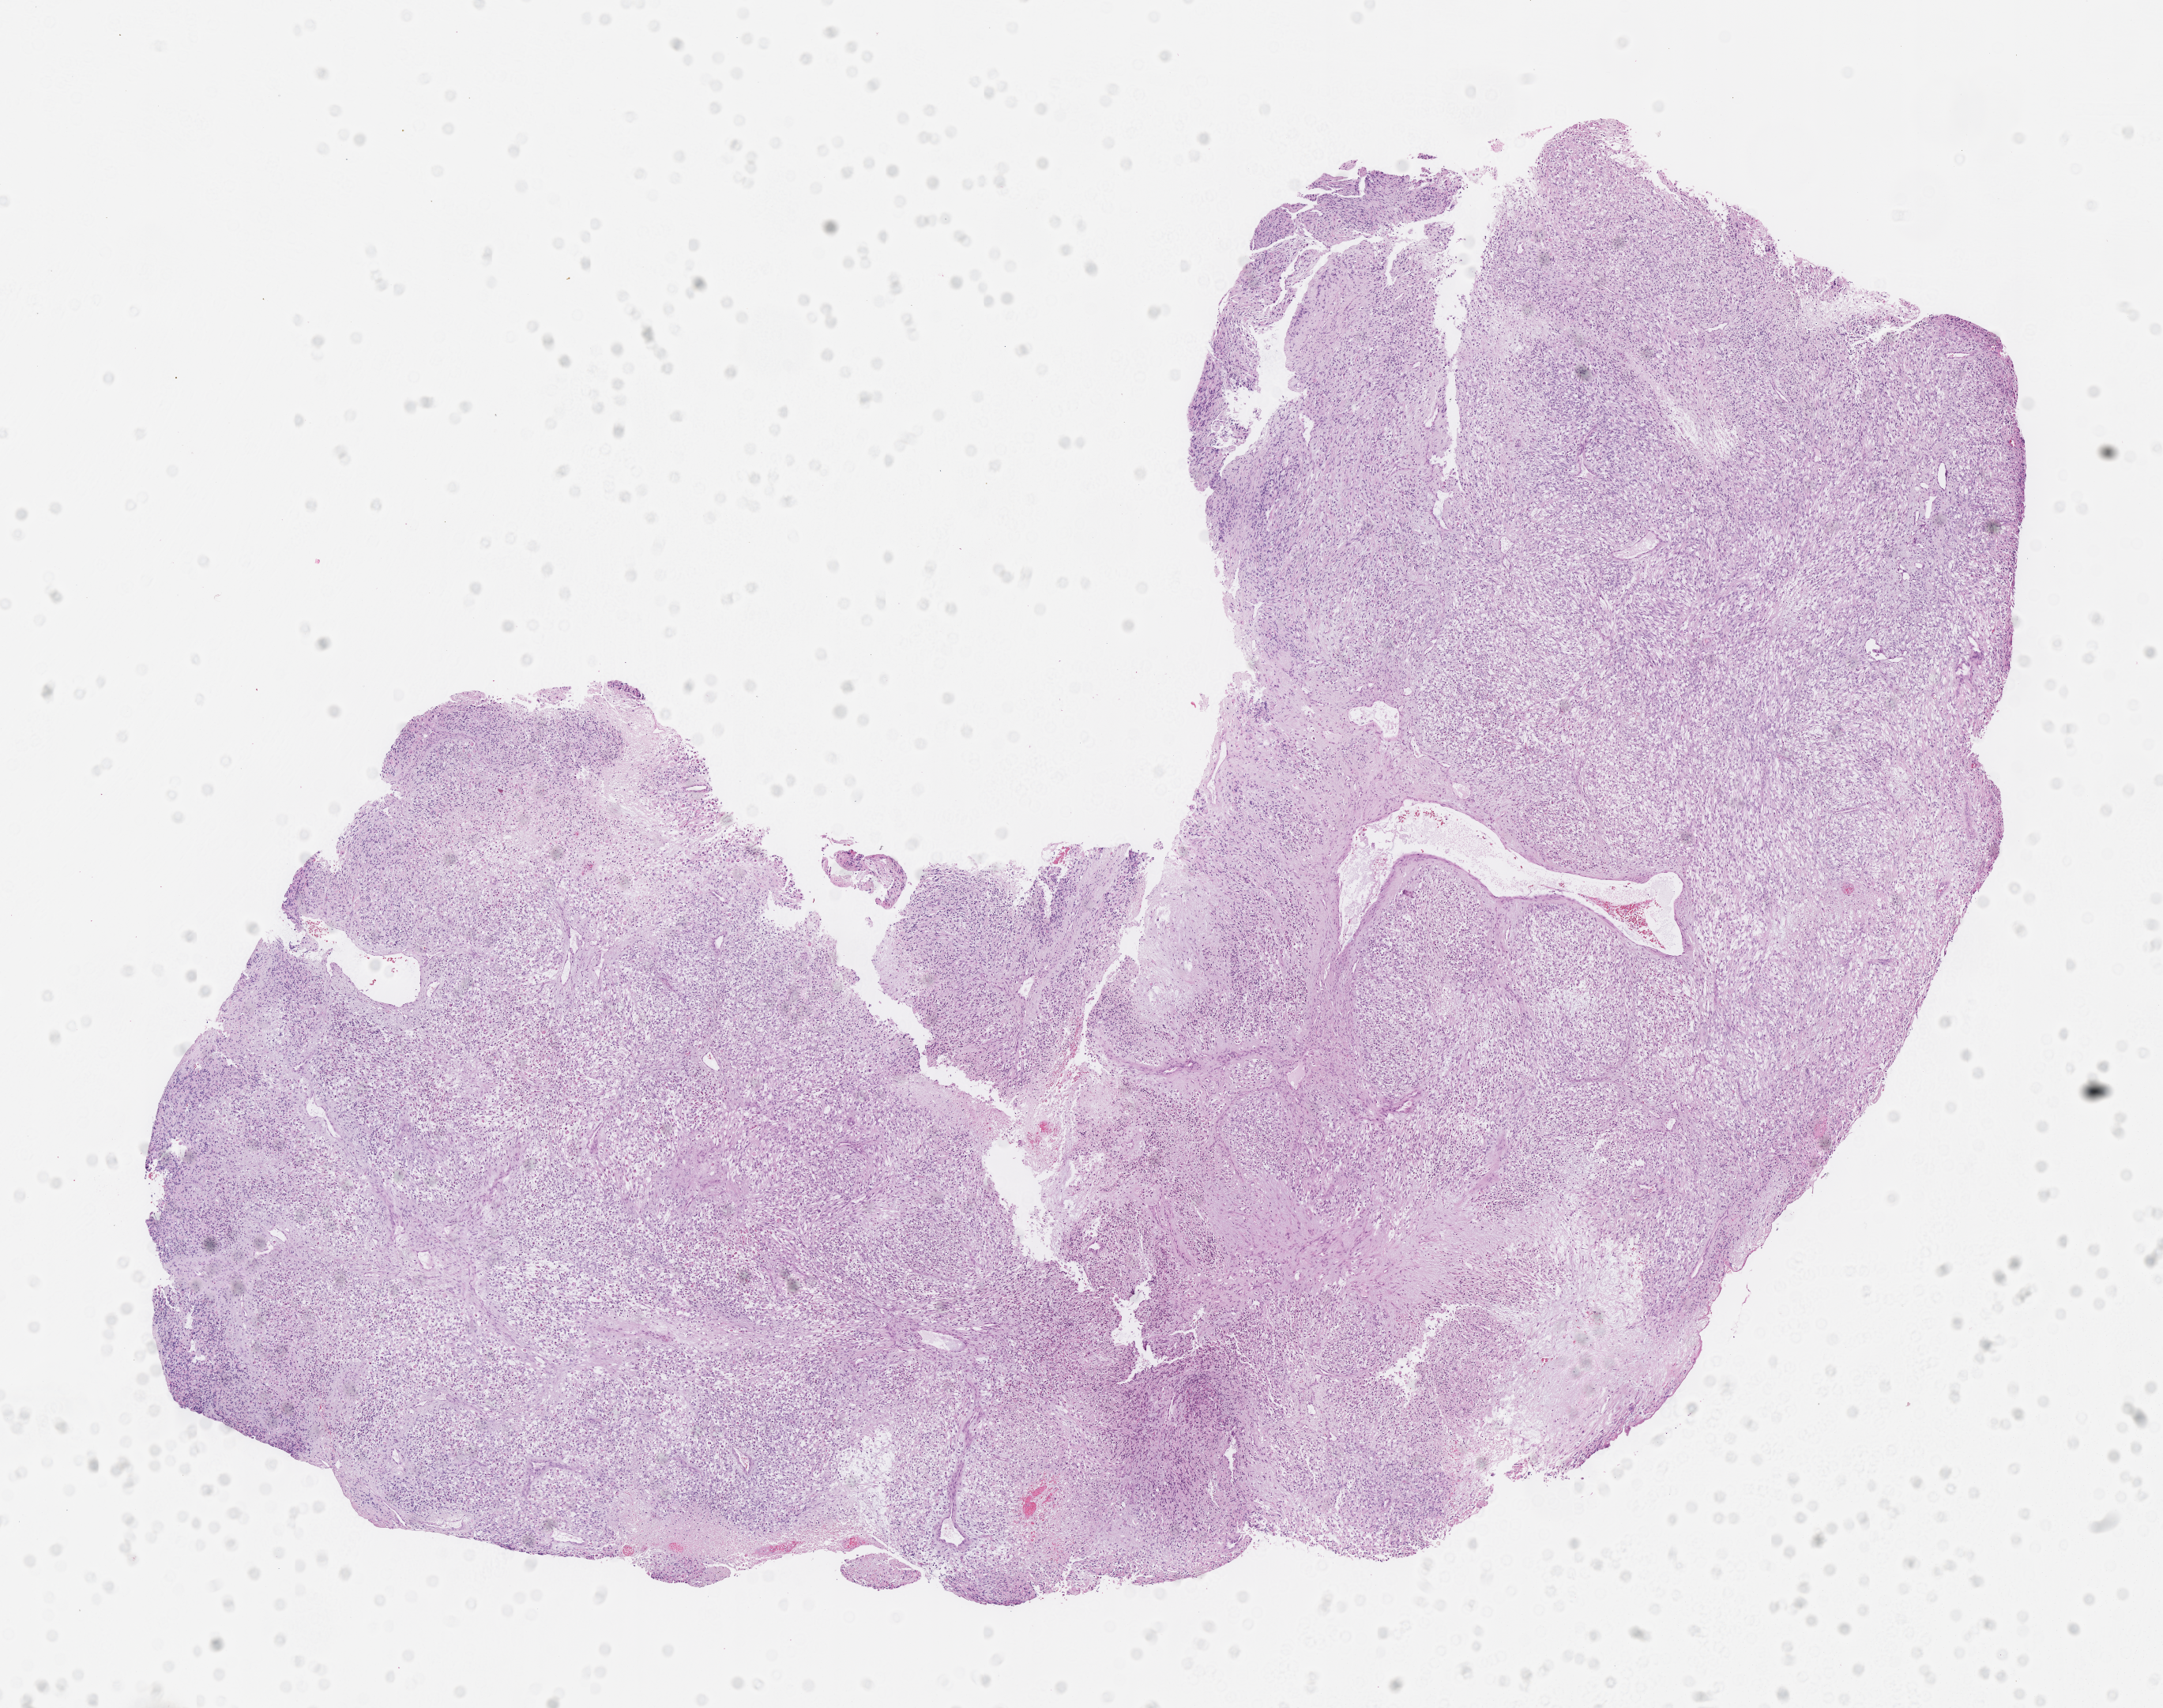
Haematoxylin and eosin whole-slide image of tumor tissue, a low-resolution overview of the entire scanned area, about 11.1 x 8.7 mm, formalin-fixed paraffin-embedded section, sample anatomic site: soft tissue, retroperitoneum. Female patient, age at diagnosis 4.8 years.
• metastatic status at presentation (as recorded): non-metastatic
• diagnosis: rhabdomyosarcoma; histological classification: embryonal rhabdomyosarcoma
• stage (as recorded): 3